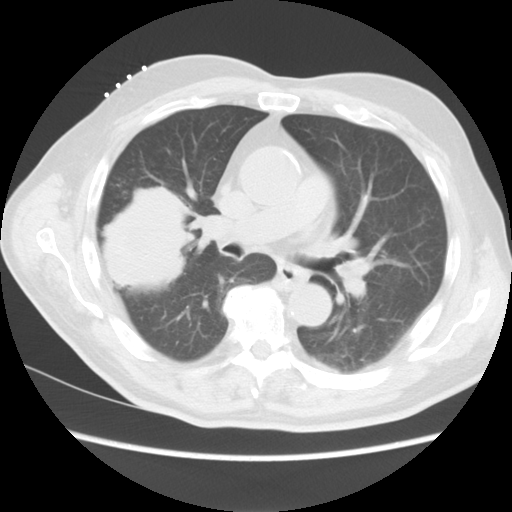
Chest CT, one axial slice. Reconstruction kernel STANDARD. 120 kVp. Lung window (W 1500 / L -600 HU). 512 × 512 image matrix, field of view 350 × 350 mm. Patient: male, 68 years. Case-level facts recorded for this patient, not image findings: clinical TNM (as recorded): T4 N3 M0.
Outlined on this slice (bounding box drawn by a radiologist):
- lung tumour (recorded histology: squamous cell carcinoma): bounding box <94,175,189,294> (left, top, right, bottom; pixels)